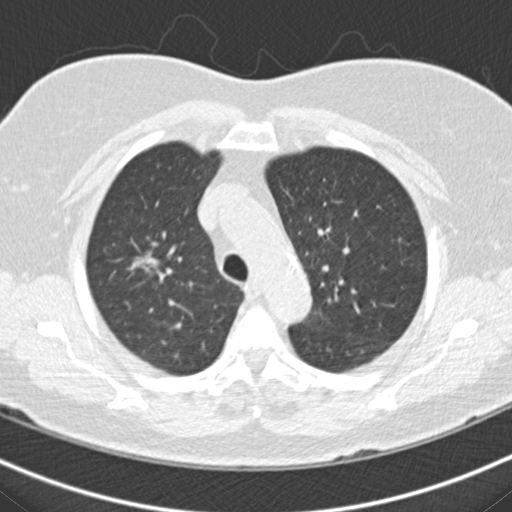
Low-dose screening chest CT, one axial slice; position 132 of 160 along the scan axis; reconstruction kernel B30f; lung window (W 1500 / L -600 HU); 2 mm slice thickness; 512 × 512 image matrix.
Structures marked on this image (outlined manually by an expert reader):
- lesion 3 (nodule, upper lobe of right lung): bounding box [x1, y1, x2, y2] px = [137, 255, 157, 271]